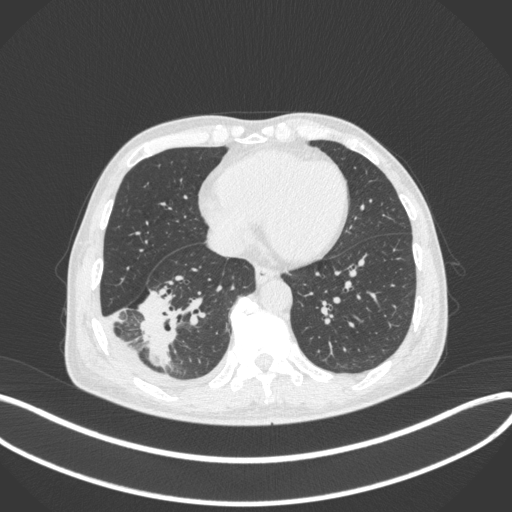
Chest CT, one axial slice; position 128 of 385 along the scan axis; 120 kVp; lung window (W 1500 / L -600 HU); 1 mm slice thickness; 512 × 512 image matrix, field of view 400 × 400 mm. Male patient, age 64 years. From the clinical record (not read from this slice): clinical TNM (as recorded): T3 N0 M0.
Structures marked on this image (rectangle marked by the reading radiologist):
- lung tumour (recorded histology: adenocarcinoma): box from (x=135, y=283) to (x=179, y=371) px